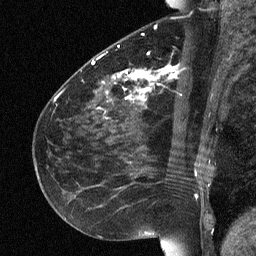
Breast MRI (dynamic contrast-enhanced), one sagittal slice; slice 28 of 64 in the series (ordered by position); dynamic contrast-enhanced study with each time point stored as its own series, time point 2 of 3 at this slice position (early post-contrast, ordered by acquisition time); 1.5 T; TE 4.8 ms, TR 27 ms; 2 mm slice thickness; 256 × 256 image matrix, field of view 180 × 180 mm. Female patient, age 51 years. Case-level facts recorded for this patient, not image findings: setting: breast cancer imaged before/during neoadjuvant chemotherapy; receptor status: HR-positive, HER2-negative.
Outlined on this slice (semi-automatic segmentation, software-assisted and operator-edited):
- analysis volume of interest (the breast-tissue region the enhancement analysis was run in; not a lesion): bounding box <72,34,182,118> (left, top, right, bottom; pixels)
- tumour enhancement mask (voxels above the 90 % enhancement threshold inside the analysis volume of interest): <92,61,173,102>